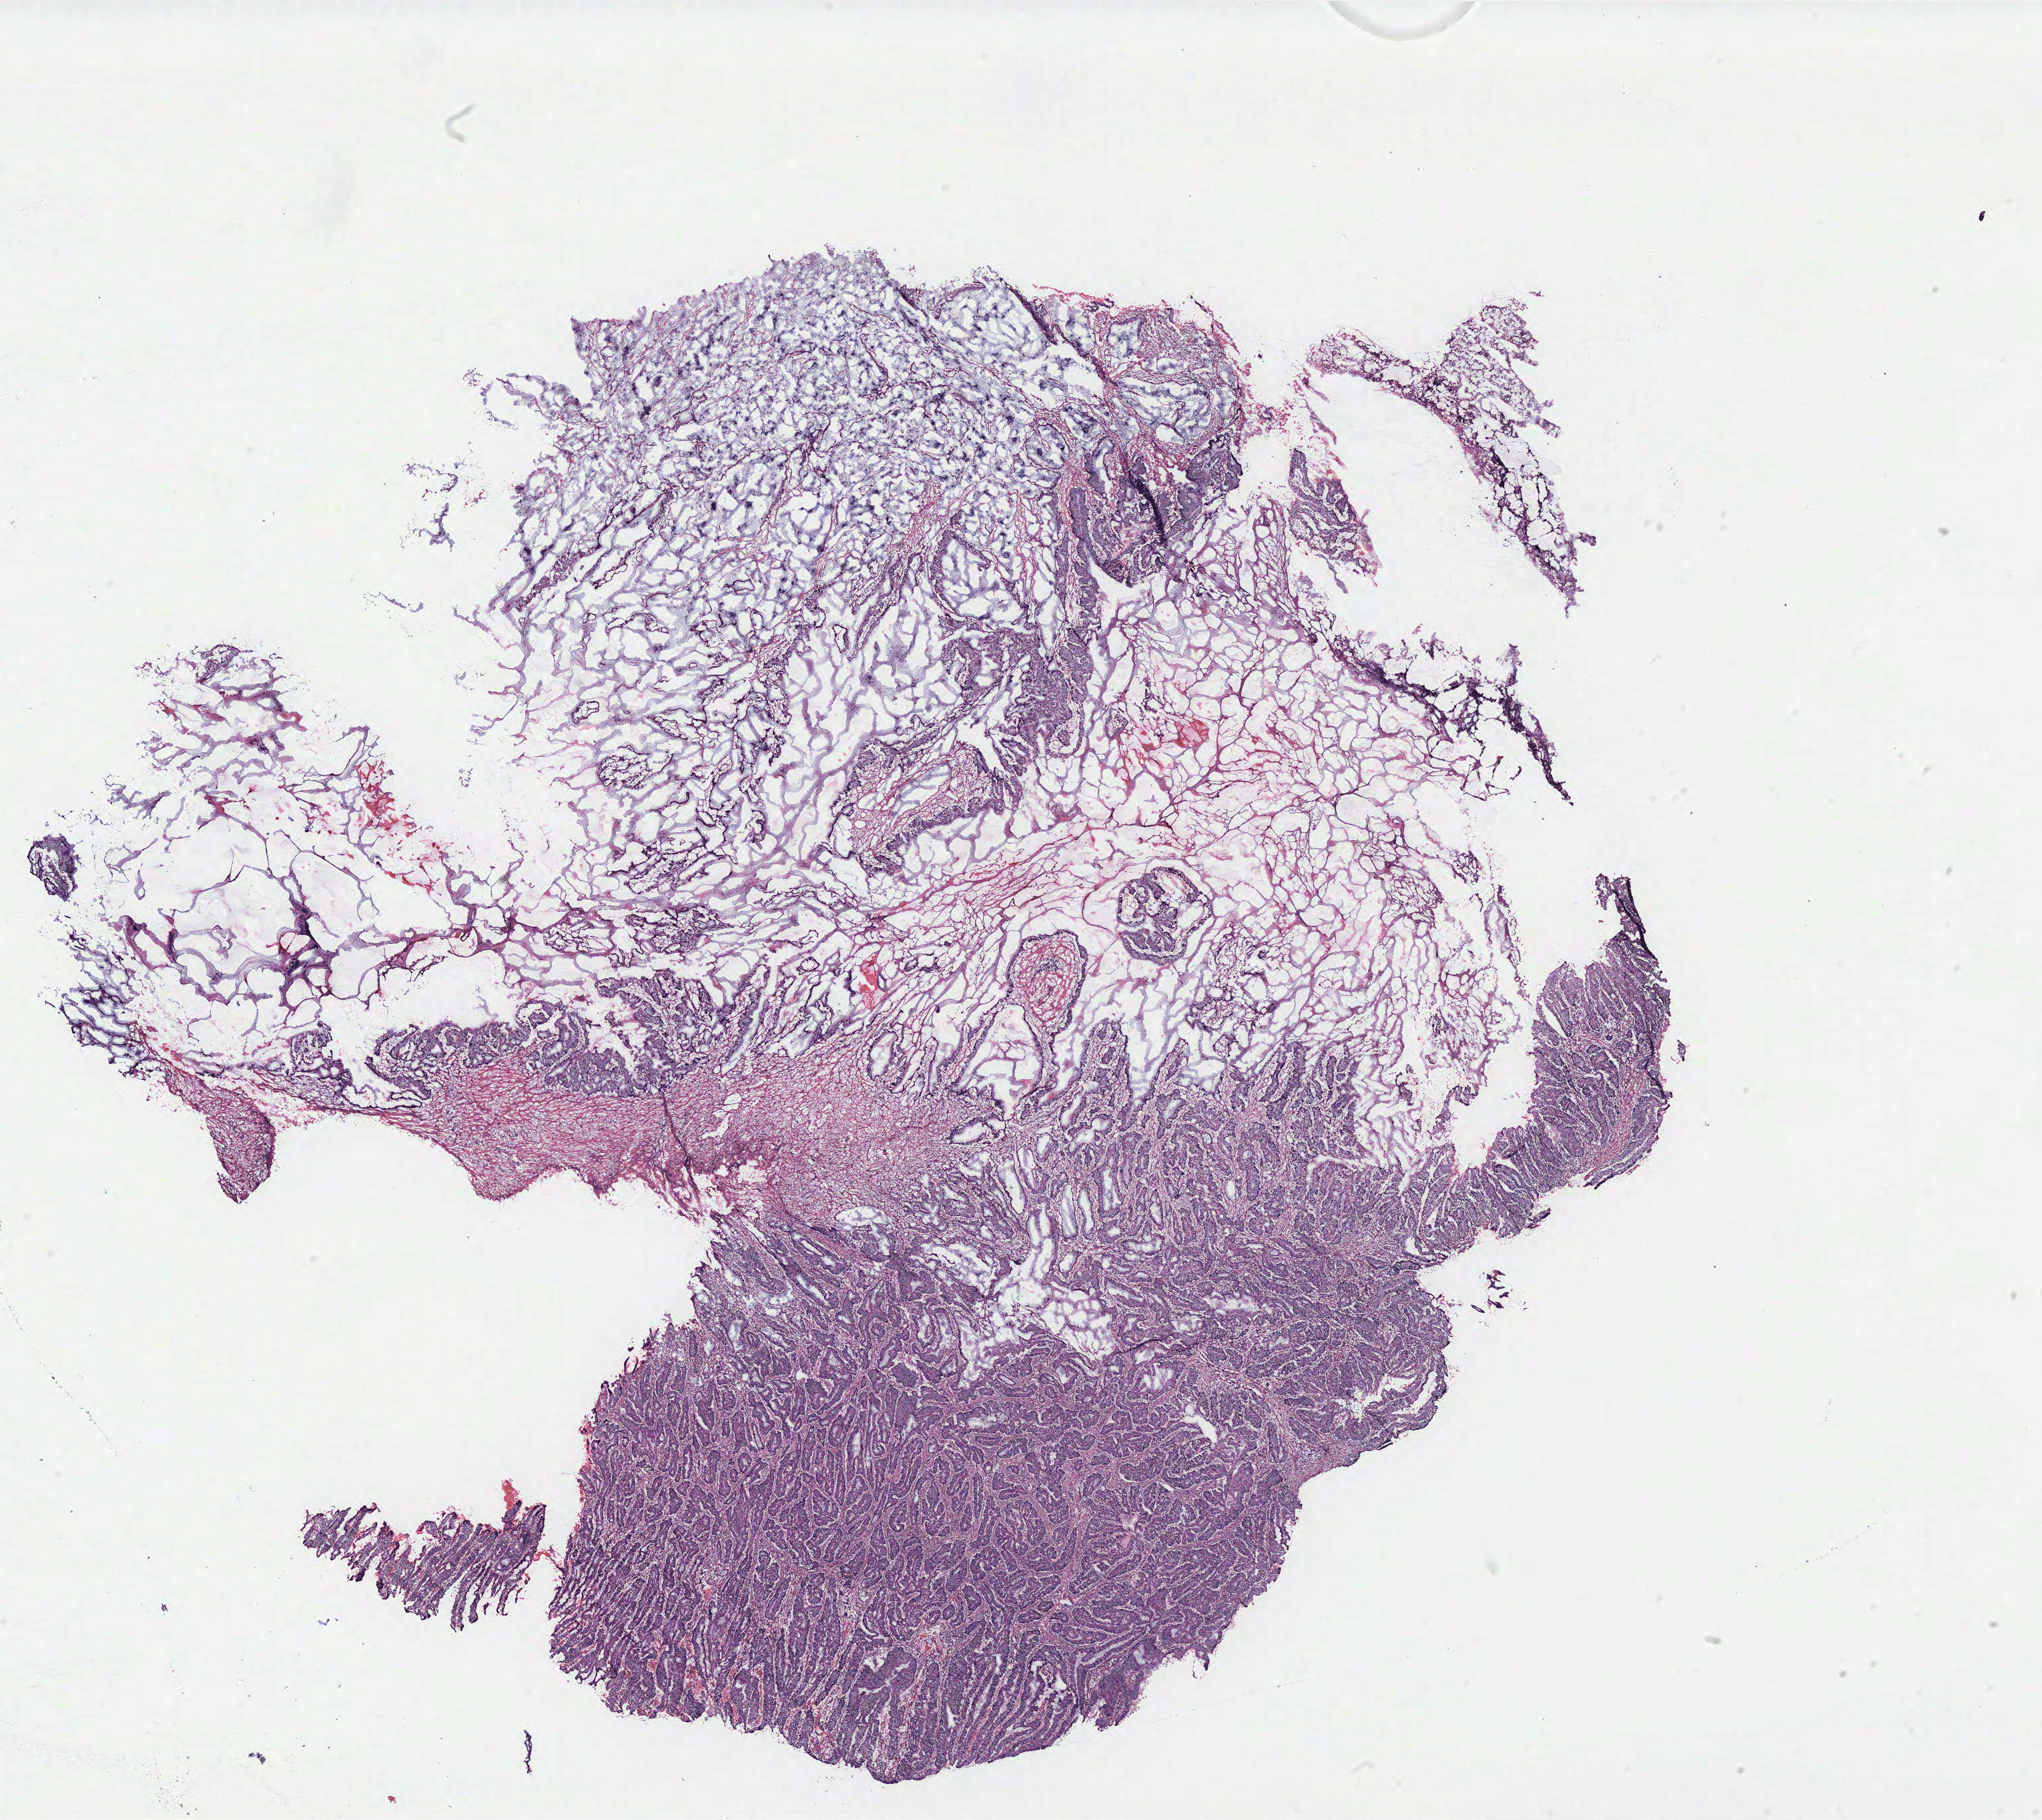
Hematoxylin and eosin (H&E) stained whole-slide image, low-resolution overview of the scanned area, about 24.5 x 21.8 mm (from a 40x scan), normal (non-tumour) tissue sample, colon. Patient: female, age 66 years.
• this section: normal (non-tumour) tissue from the same patient
• patient diagnosis: Adenocarcinoma, NOS